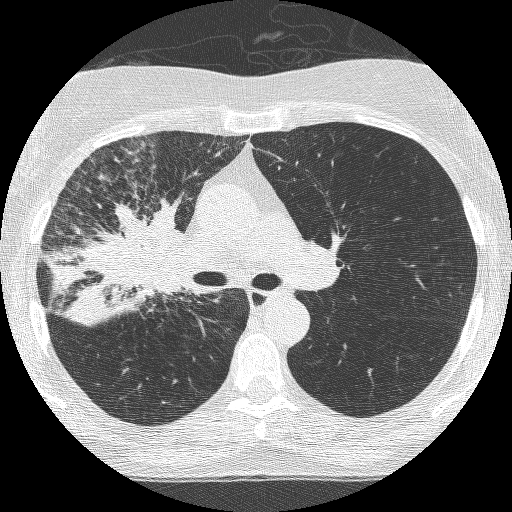
Axial slice from a low-dose chest CT screening exam; third annual screen; lung window (W 1500 / L -600 HU); 512 × 512 image matrix. Female participant, aged 64 years at enrolment.
Expert-annotated lung lesion, bounding box <80,204,204,328> (left, top, right, bottom; pixels). The exam's reader record, not a measurement of the box and not confirmed to be the same lesion: non-calcified nodule or mass ≥4 mm, right upper lobe, 49 × 43 mm, spiculated (stellate) margins, soft tissue attenuation, pre-existing on the prior screen: yes; interval growth: yes. Participant outcome: lung cancer diagnosed 7 days after this screen — adenocarcinoma, NOS, right upper lobe, right middle lobe, right hilum, stage IV (AJCC 6th edition), 85 mm at pathology.